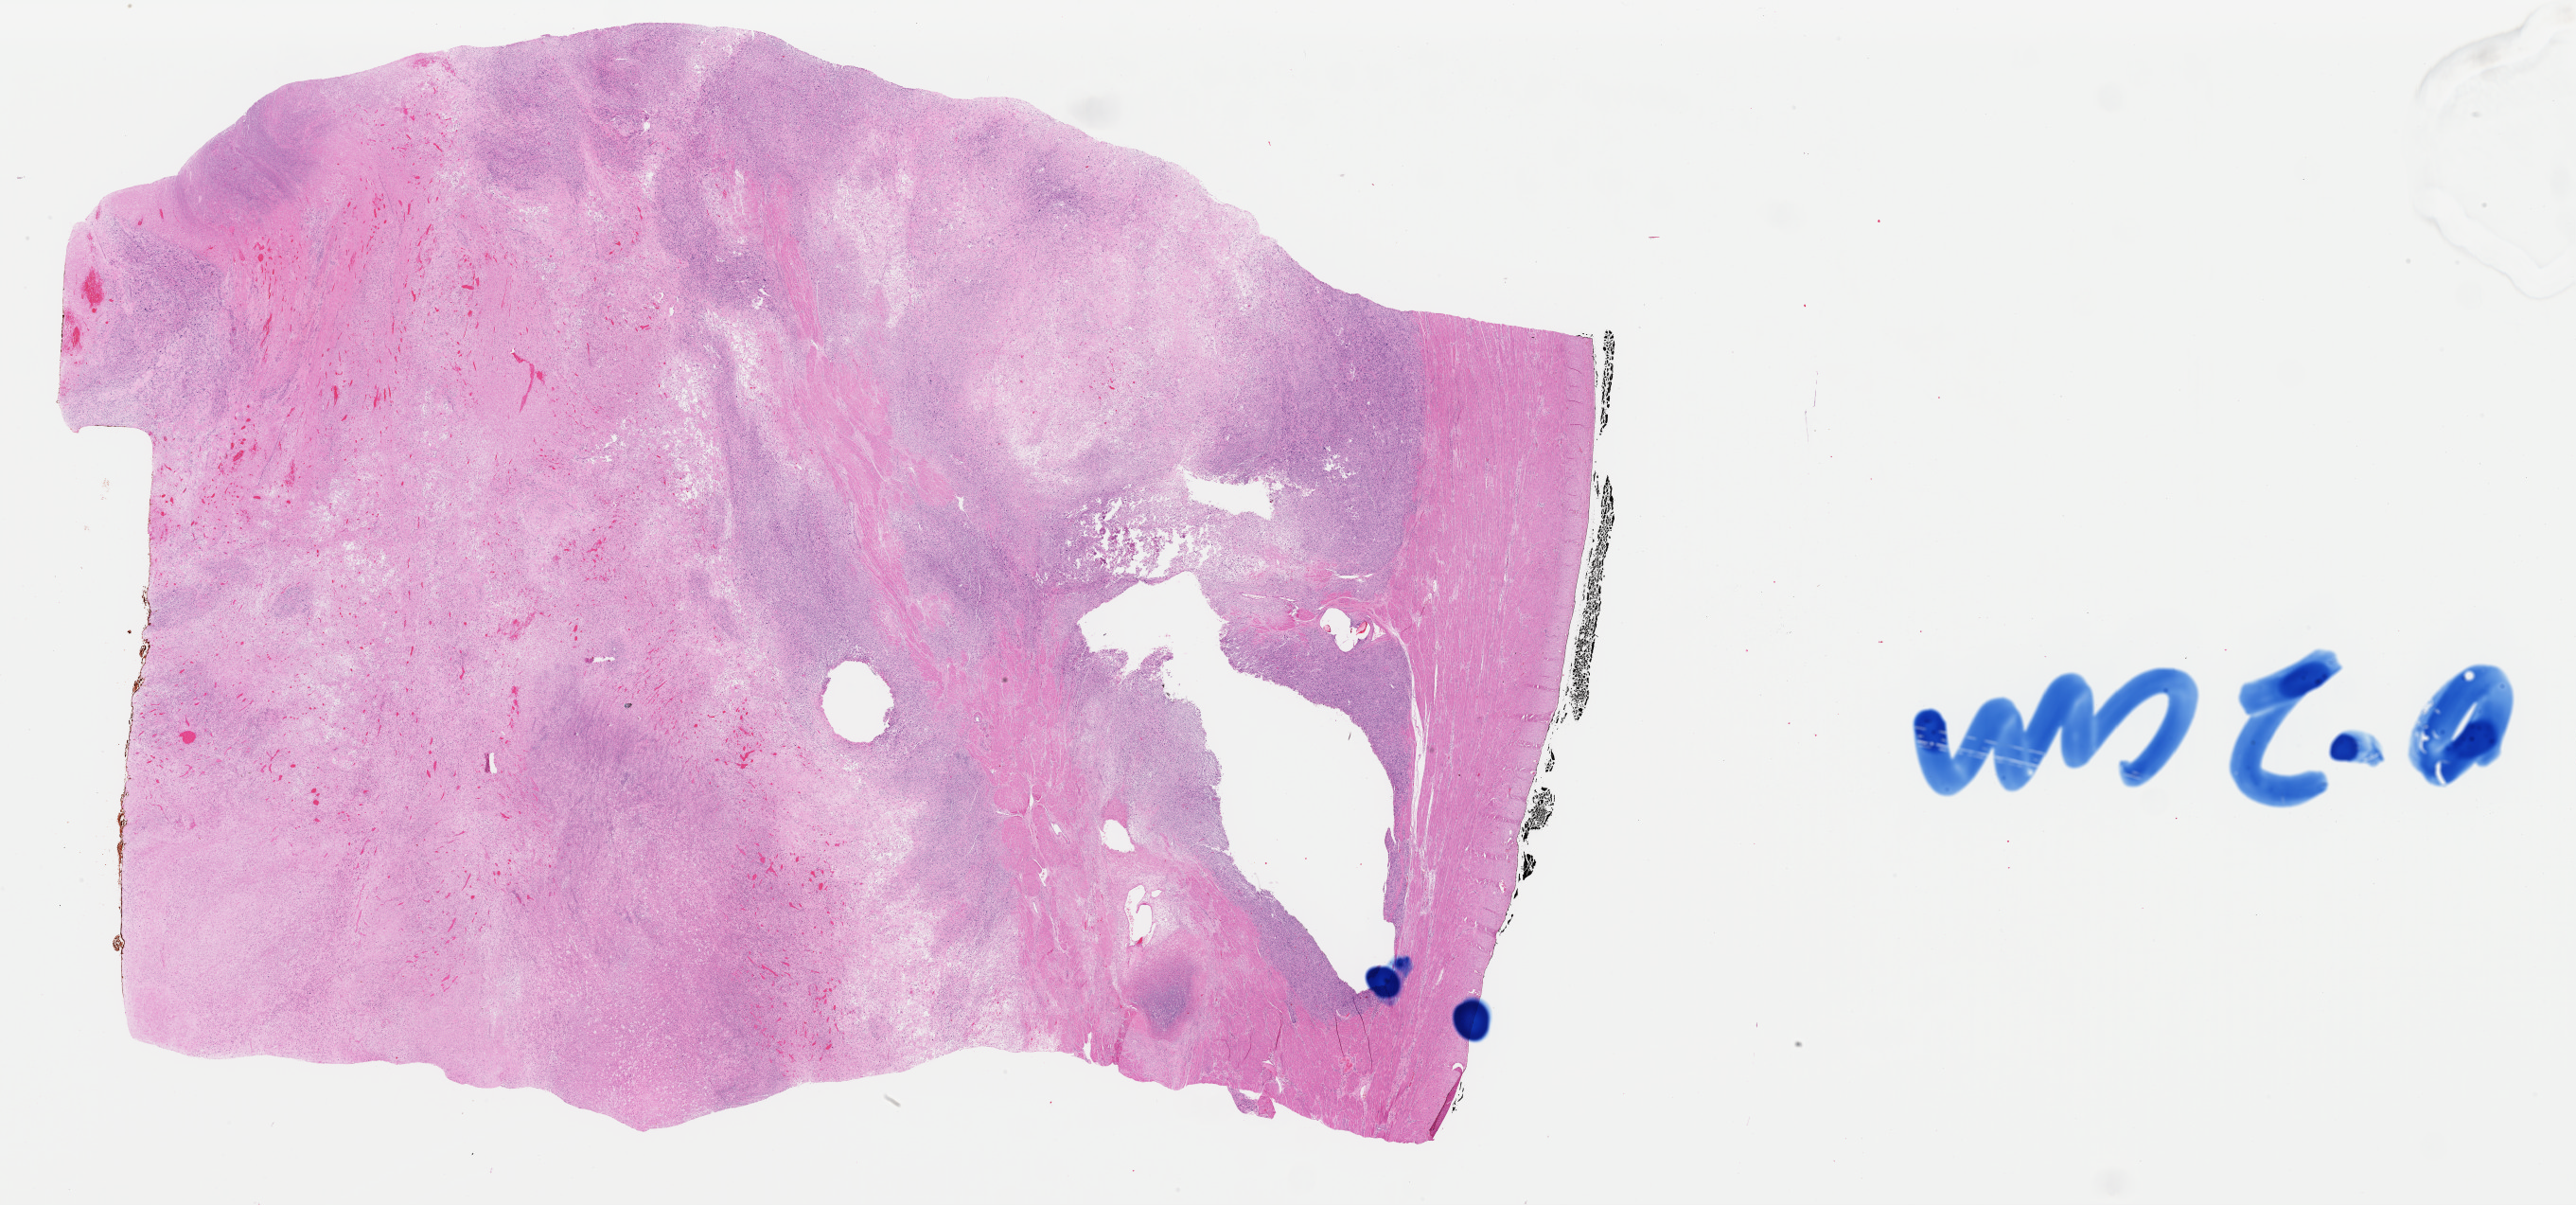
Whole-slide histology image, Hematoxylin and eosin (H&E) stained — whole scanned area (about 43.0 x 20.1 mm) shown as a low-resolution overview; FFPE section; uterus, primary tumour sample. Patient: female, age at initial diagnosis 41 years.
Diagnosis: Leiomyosarcoma, NOS.